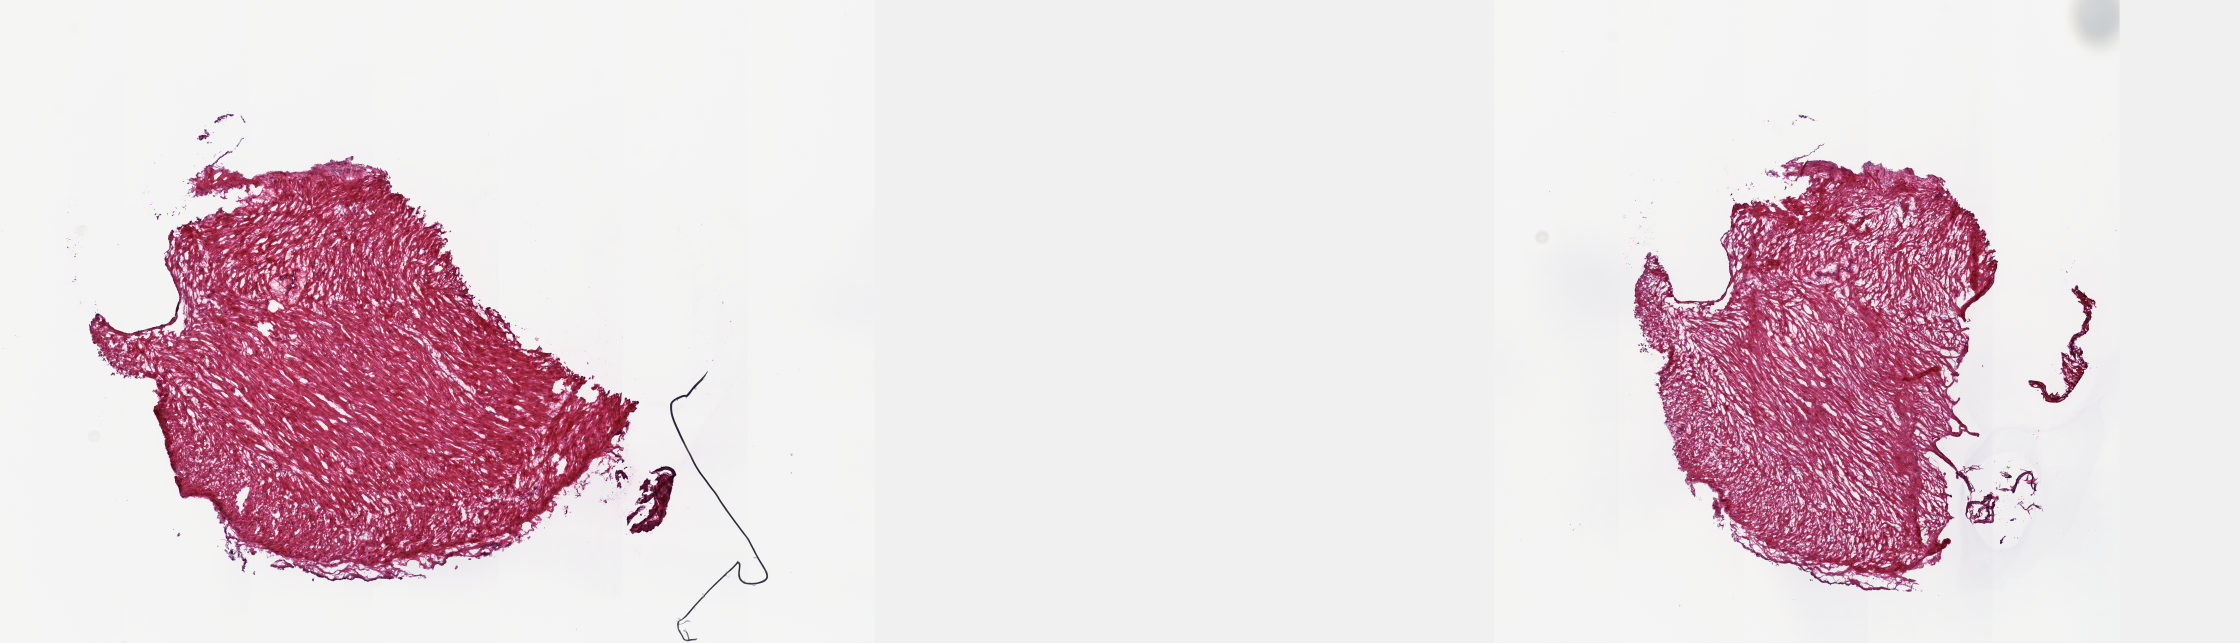
Whole-slide histology image, H&E — whole scanned area (about 18.1 x 5.2 mm, slide scanned at 20x) shown as a low-resolution overview; frozen section; sample: solid tissue normal (non-tumour tissue), prostate. Patient: male, age at initial diagnosis 58 years. Composition of this section per pathologist review: tumour cells 0%, tumour nuclei 0%, normal cells 100%, stromal cells 0%, necrosis 0%. Inflammatory infiltration, as recorded: lymphocyte infiltration 1%, monocyte infiltration 0%, neutrophil infiltration 0%.
This section: solid tissue normal sample (biorepository sample class). Patient diagnosis: Adenocarcinoma, NOS (prostate gland).